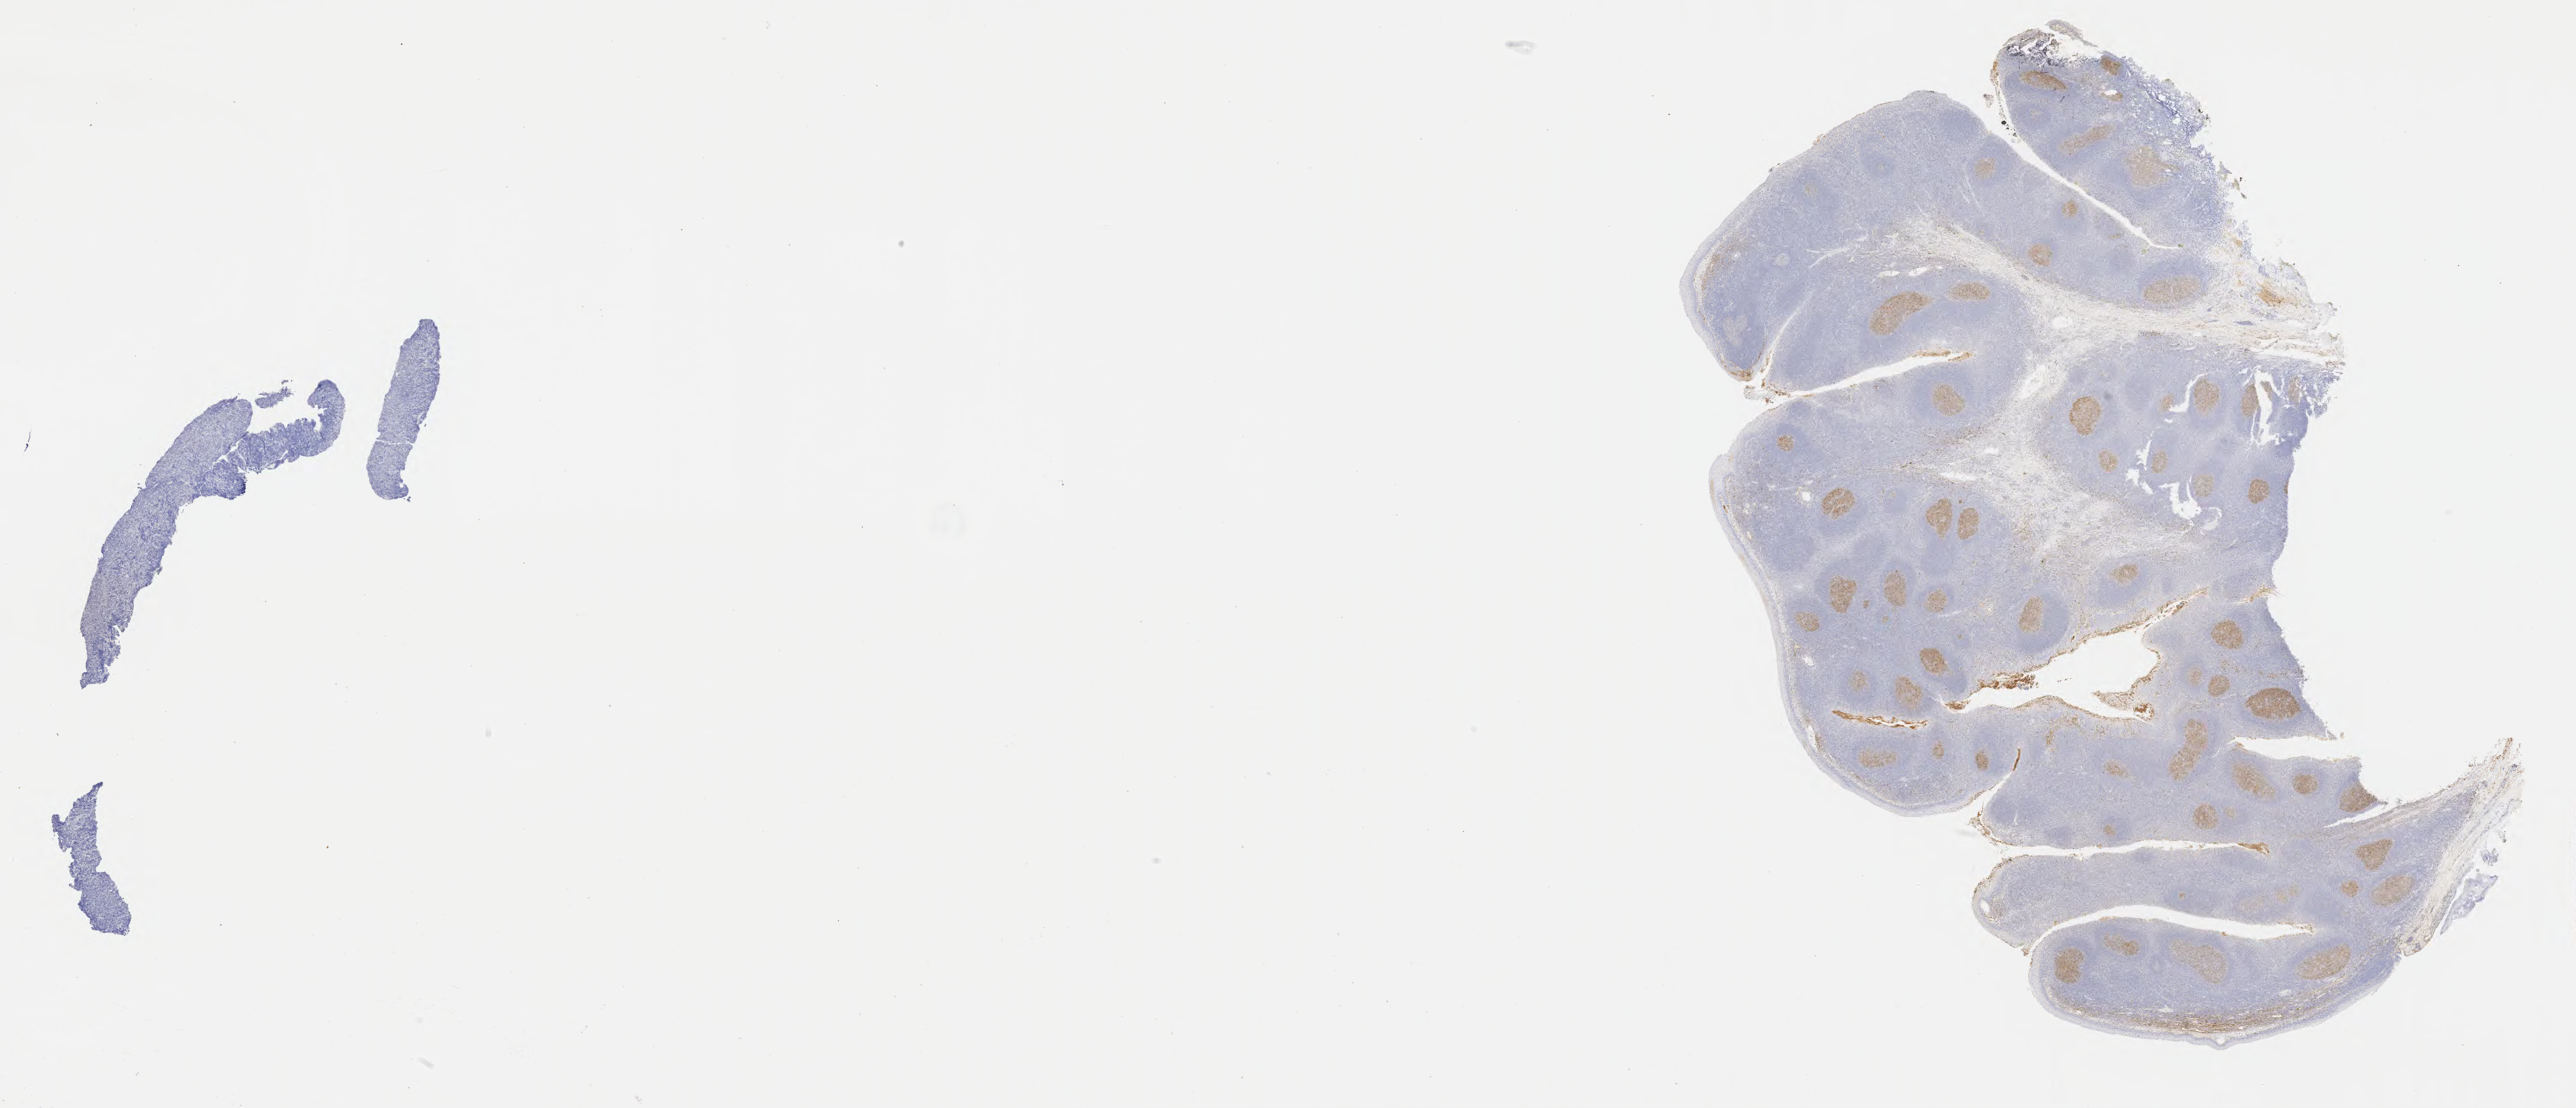
Whole-slide image, immunohistochemical stain for CD10, whole scanned area (about 31.7 x 13.6 mm) shown as a low-resolution overview; specimen: tumor tissue. Patient male; 10 years old.
Histologic diagnosis: Diffuse large B-cell lymphoma, NOS.